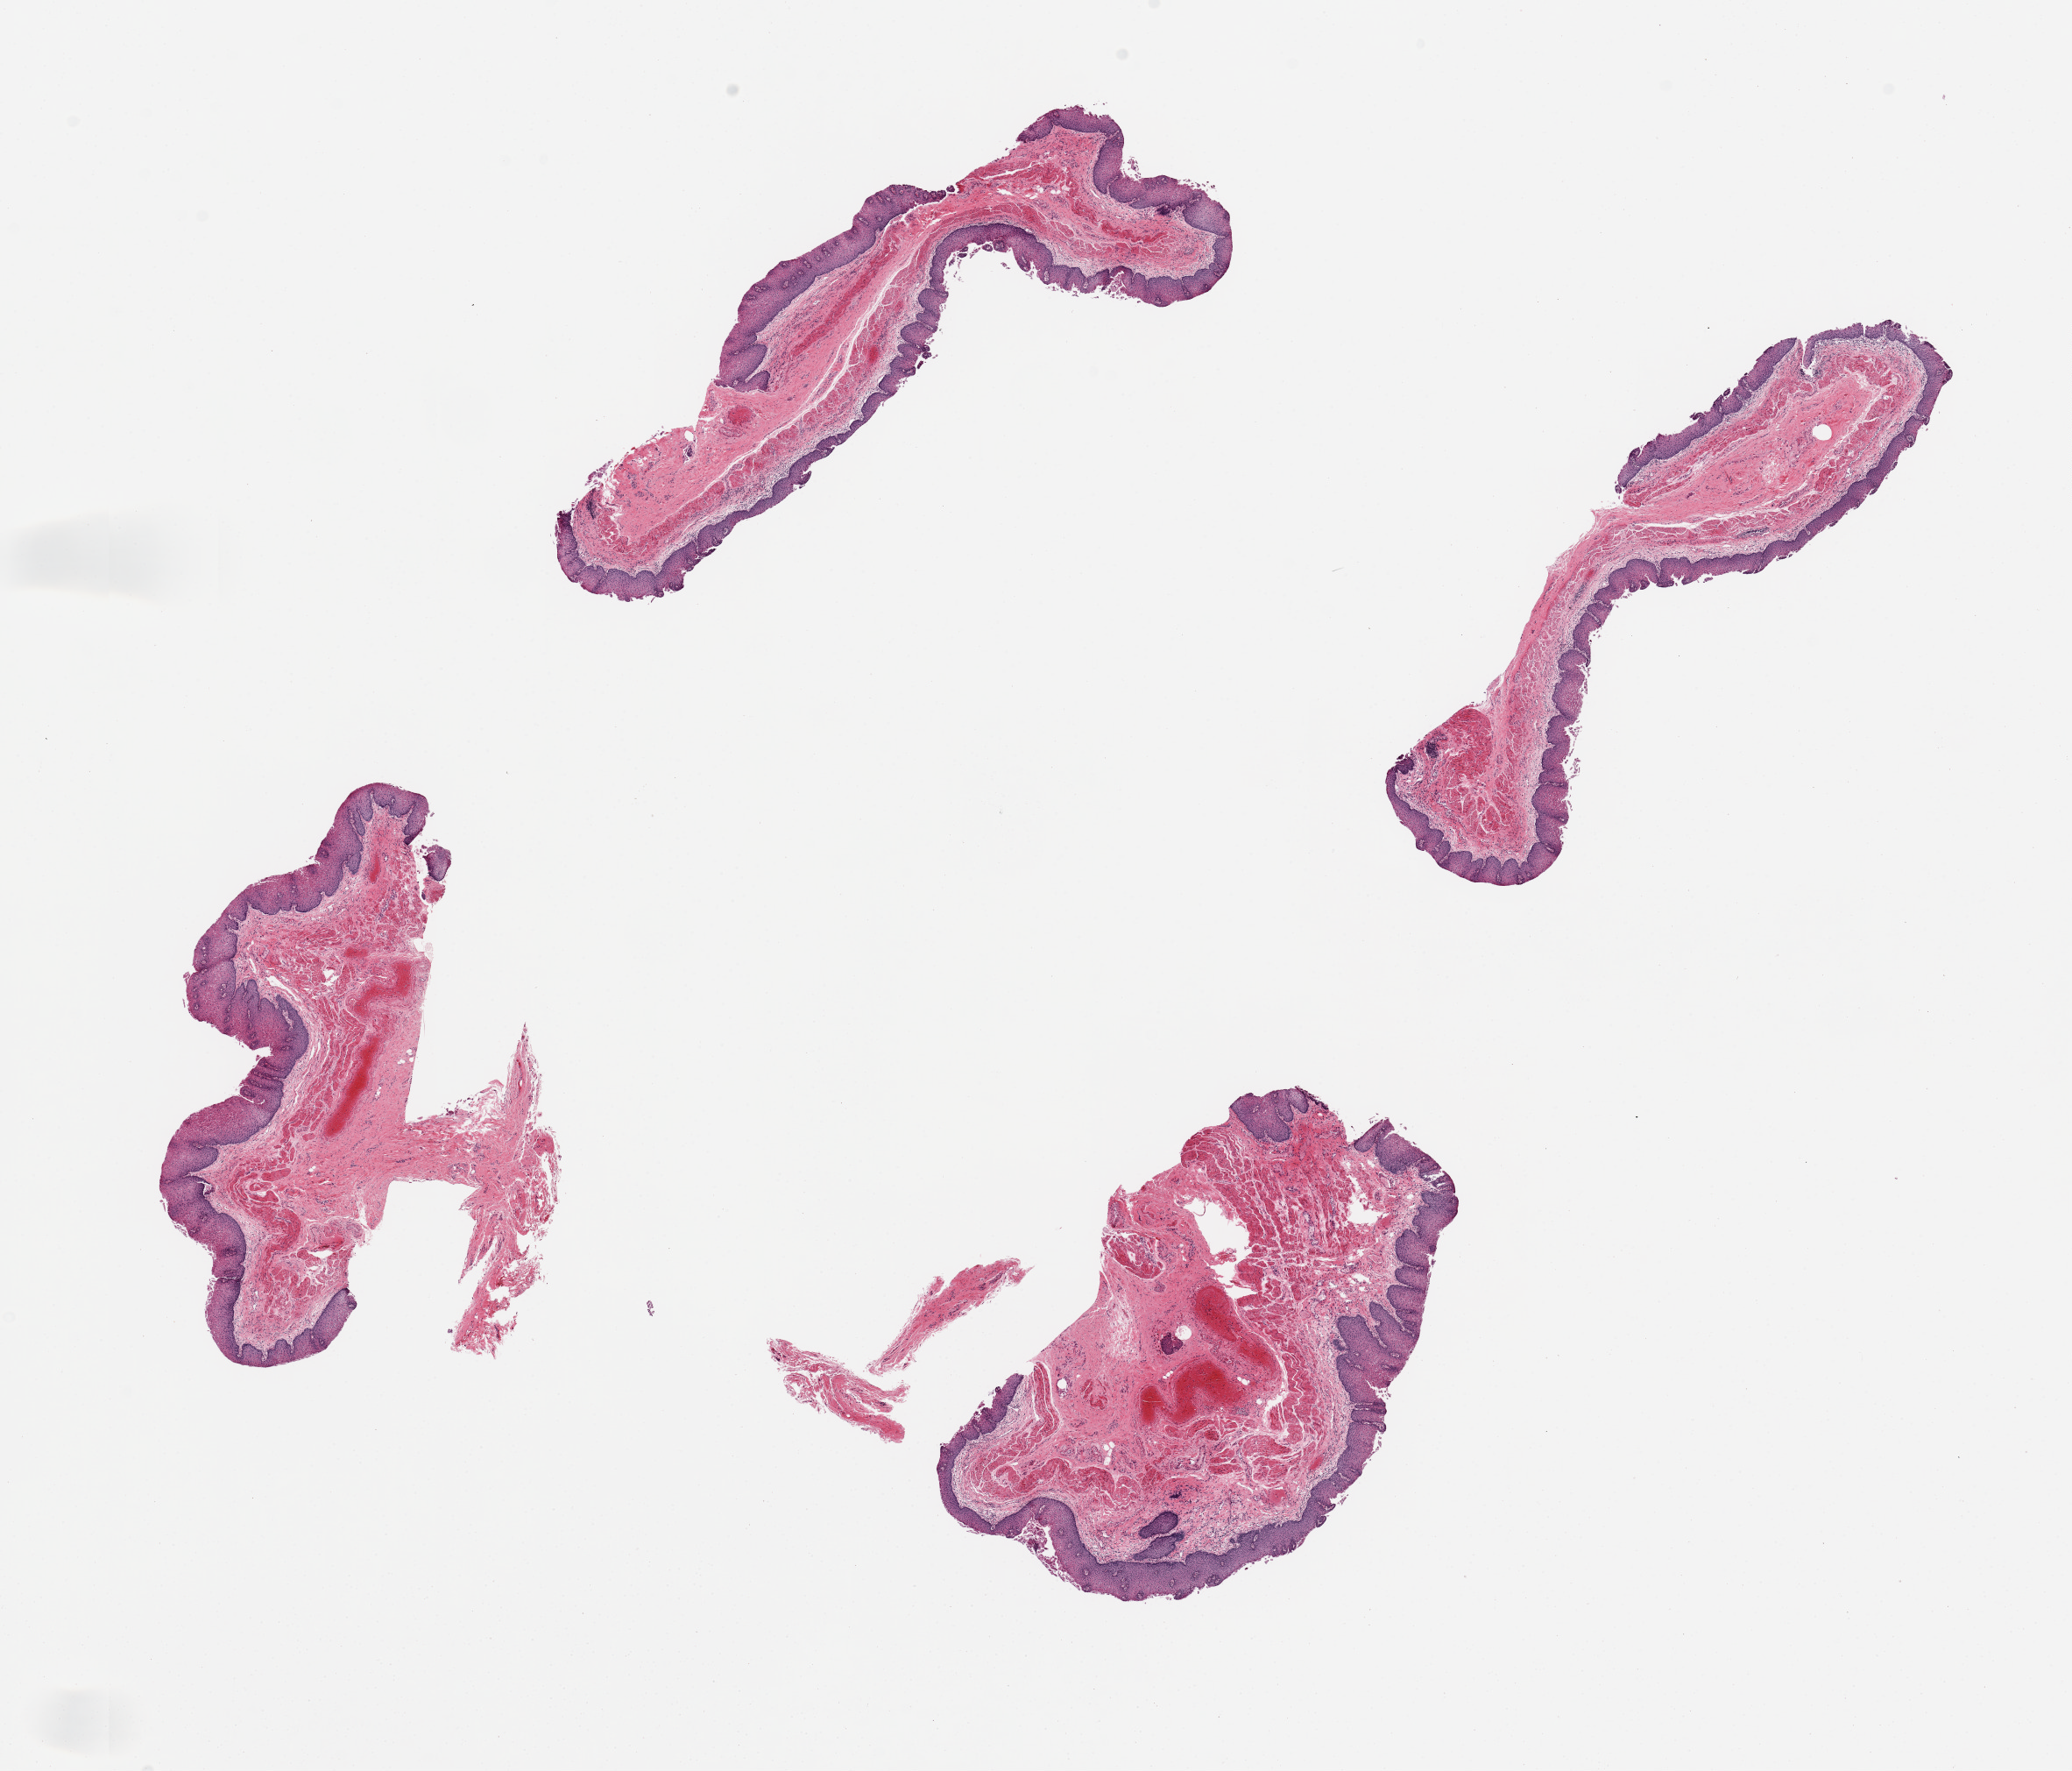
Digitized haematoxylin and eosin-stained section, whole scanned area (about 18.7 x 16.0 mm, acquisition: 20x scan) shown as a low-resolution overview, PAXgene-fixed paraffin-embedded (PFPE) section, section of esophageal mucous membrane (target tissue), donor tissue sample. Donor sex: male.
Pathologist's review note for this sample: 4 pieces. well dissected; focal surface sloughing.